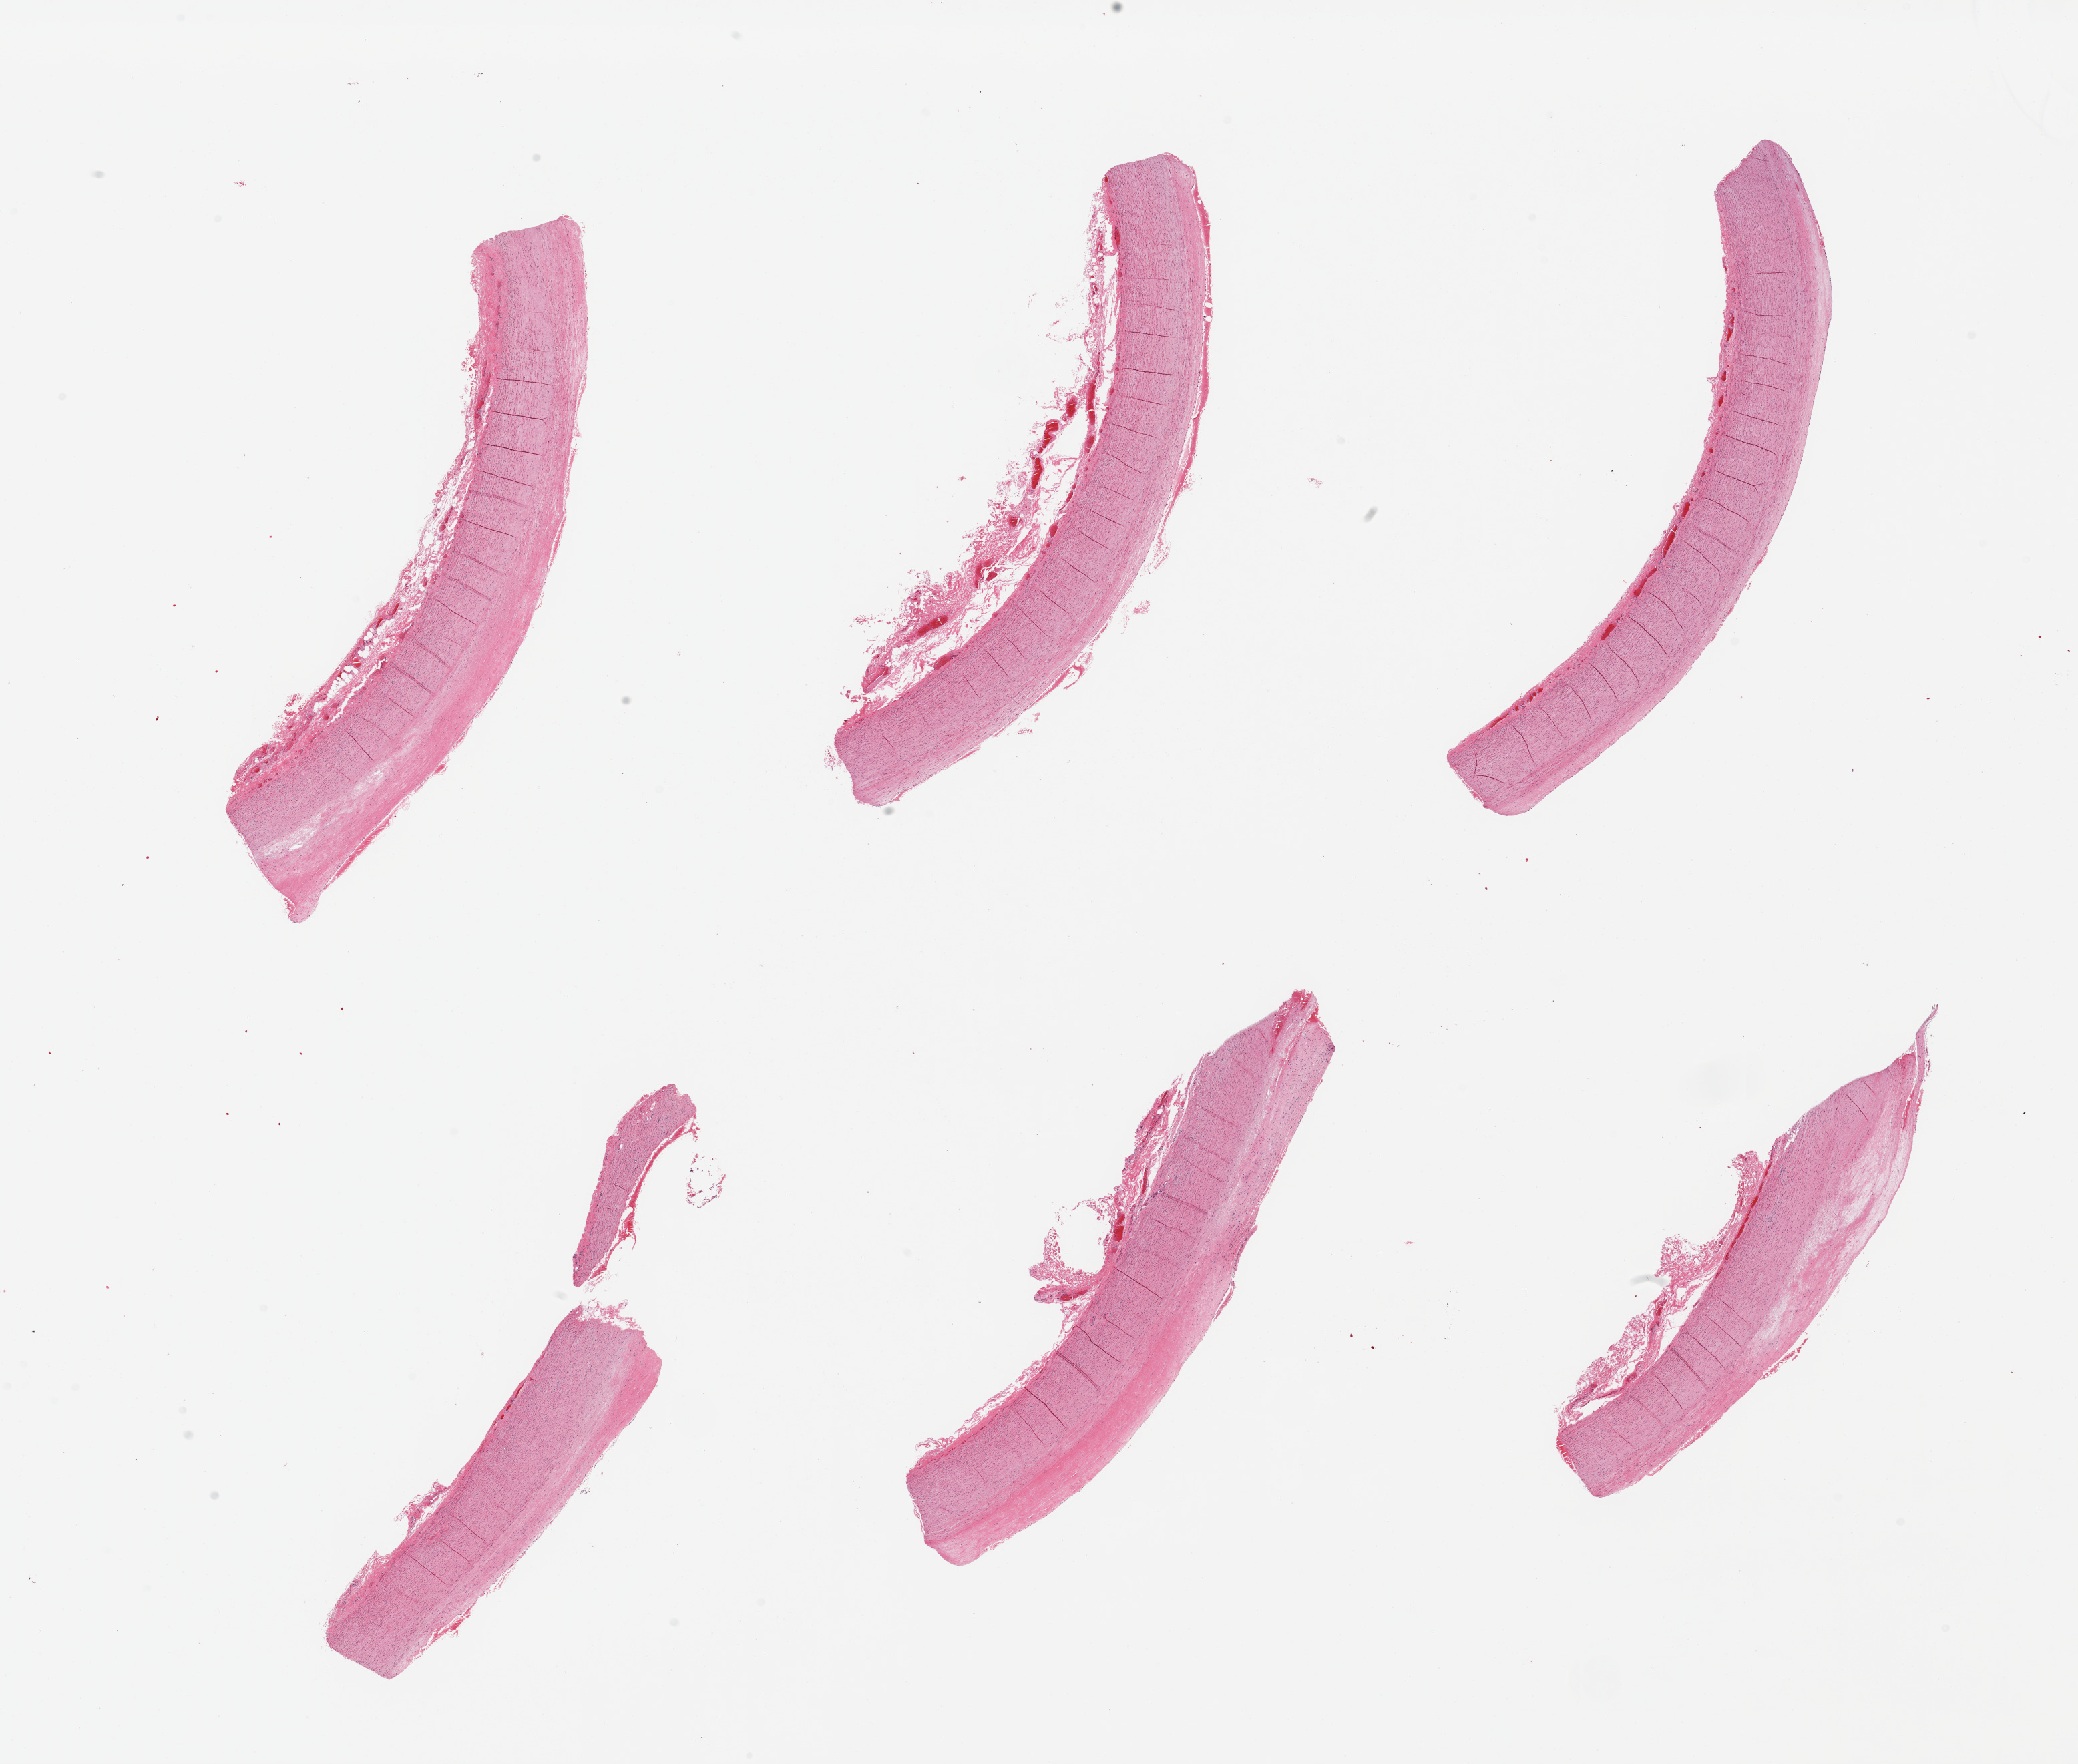
Digitized hematoxylin and eosin (H&E)-stained section, brightfield, low-resolution overview of the scanned area, about 24.6 x 20.9 mm (from a 20x scan), PAXgene-fixed paraffin-embedded (PFPE) section, section of aorta (target tissue), tissue donor sample. Male donor.
* pathologist's review note for this sample: 6 pieces, atherosis up to ~0.6mm